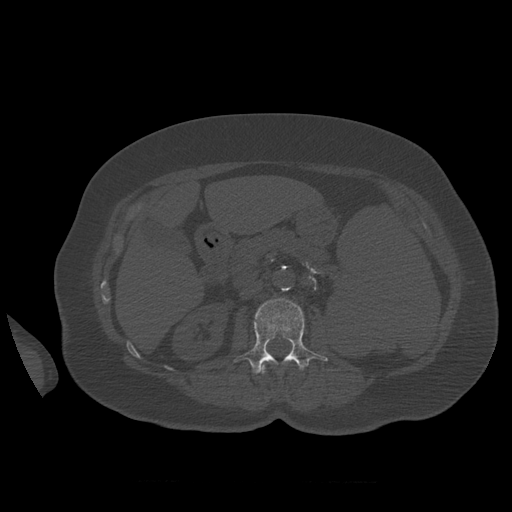
CT including the spine, one axial slice. Reconstruction kernel STANDARD. Bone window (W 1800 / L 400 HU). 1.25 mm slice thickness. 512 × 512 image matrix. Patient age 81 years. From the clinical record (not read from this slice): primary cancer: renal; vertebrae with lytic lesions (as recorded): L1.
Annotated regions visible in this slice (semi-automatically segmented with operator editing):
- L1 vertebra: bounding box (x1, y1, x2, y2) in pixels: (260, 364, 266, 374)
- L2 vertebra: (234, 298, 328, 374)